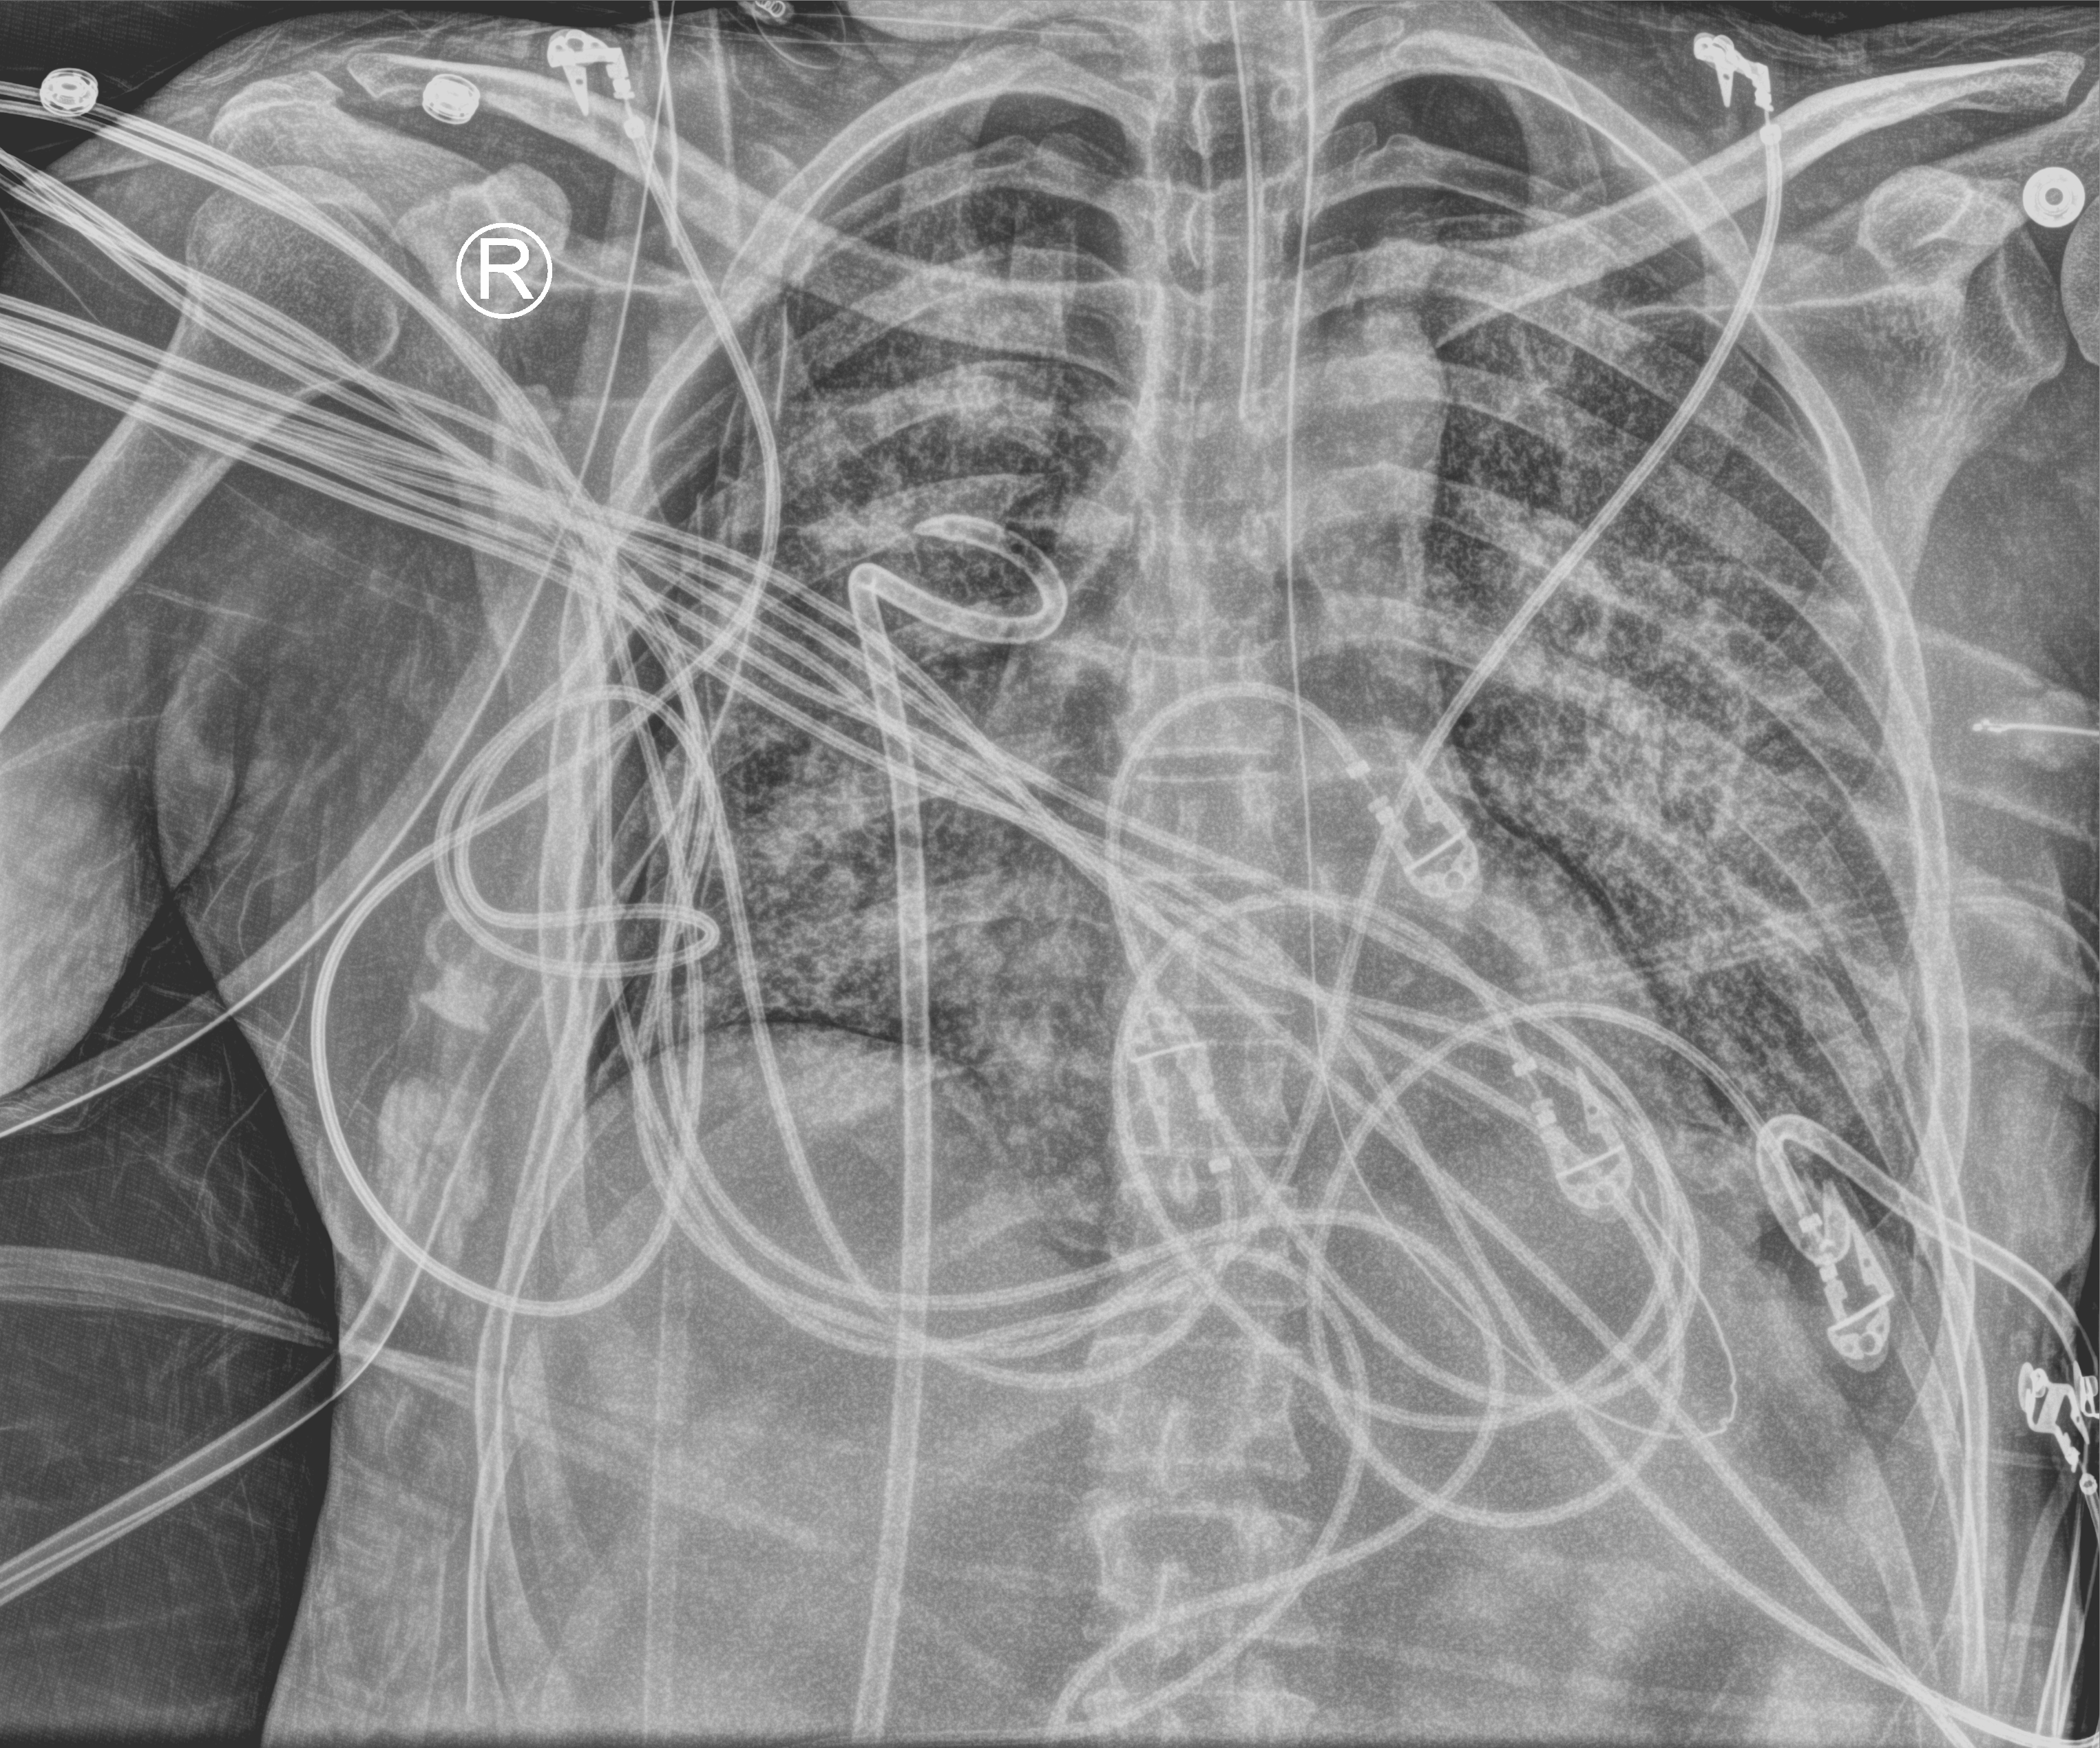
Bedside chest radiograph (computed radiography). Patient hospitalised with COVID-19, aged 18–59 years.
Hospital-stay facts (about this admission, not read from this image; timing relative to this image not recorded):
- admitted to intensive care during this hospital stay: yes
- mechanically ventilated during this hospital stay: yes